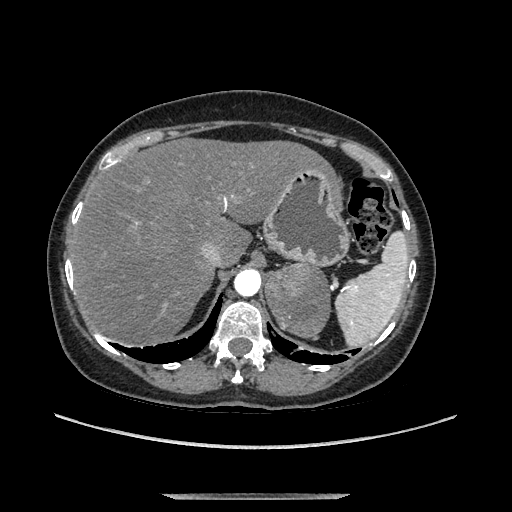
Contrast-enhanced abdominal CT, one axial slice; slice 101 of 169 in the series (ordered by position); soft-tissue window (W 400 / L 40 HU); 512 × 512 image matrix. Female patient. Case-level facts recorded for this patient, not image findings: diagnosis: adrenocortical carcinoma; tumour side: left adrenal; tumour size at pathology: 9 cm; Ki-67 index: 2 %; stage (as recorded): 3.
Structures marked on this image (semi-automatically segmented with operator editing):
- mass: bounding box (x1, y1, x2, y2) in pixels: (268, 264, 329, 338)